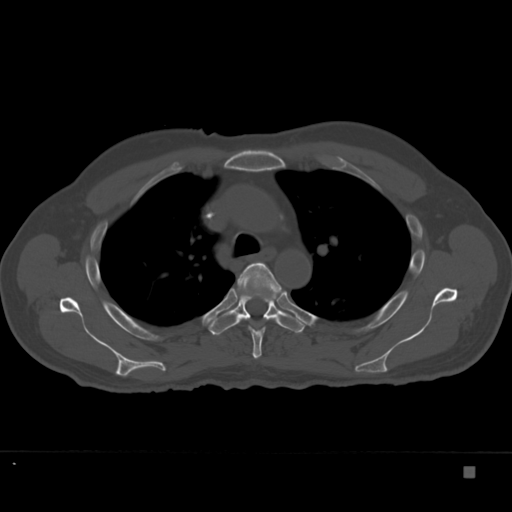
CT including the spine, one axial slice; slice 263 of 332 in the series (ordered by position); 120 kVp; bone window (W 1800 / L 400 HU); 512 × 512 image matrix, field of view 389 × 389 mm. Patient: male, 72 years. Case-level facts recorded for this patient, not image findings: primary cancer: skeletal.
Annotated regions visible in this slice (semi-automatically segmented with operator editing):
- T4 vertebra: bounding box [x1, y1, x2, y2] px = [235, 262, 284, 359]
- T5 vertebra: [208, 292, 304, 336]